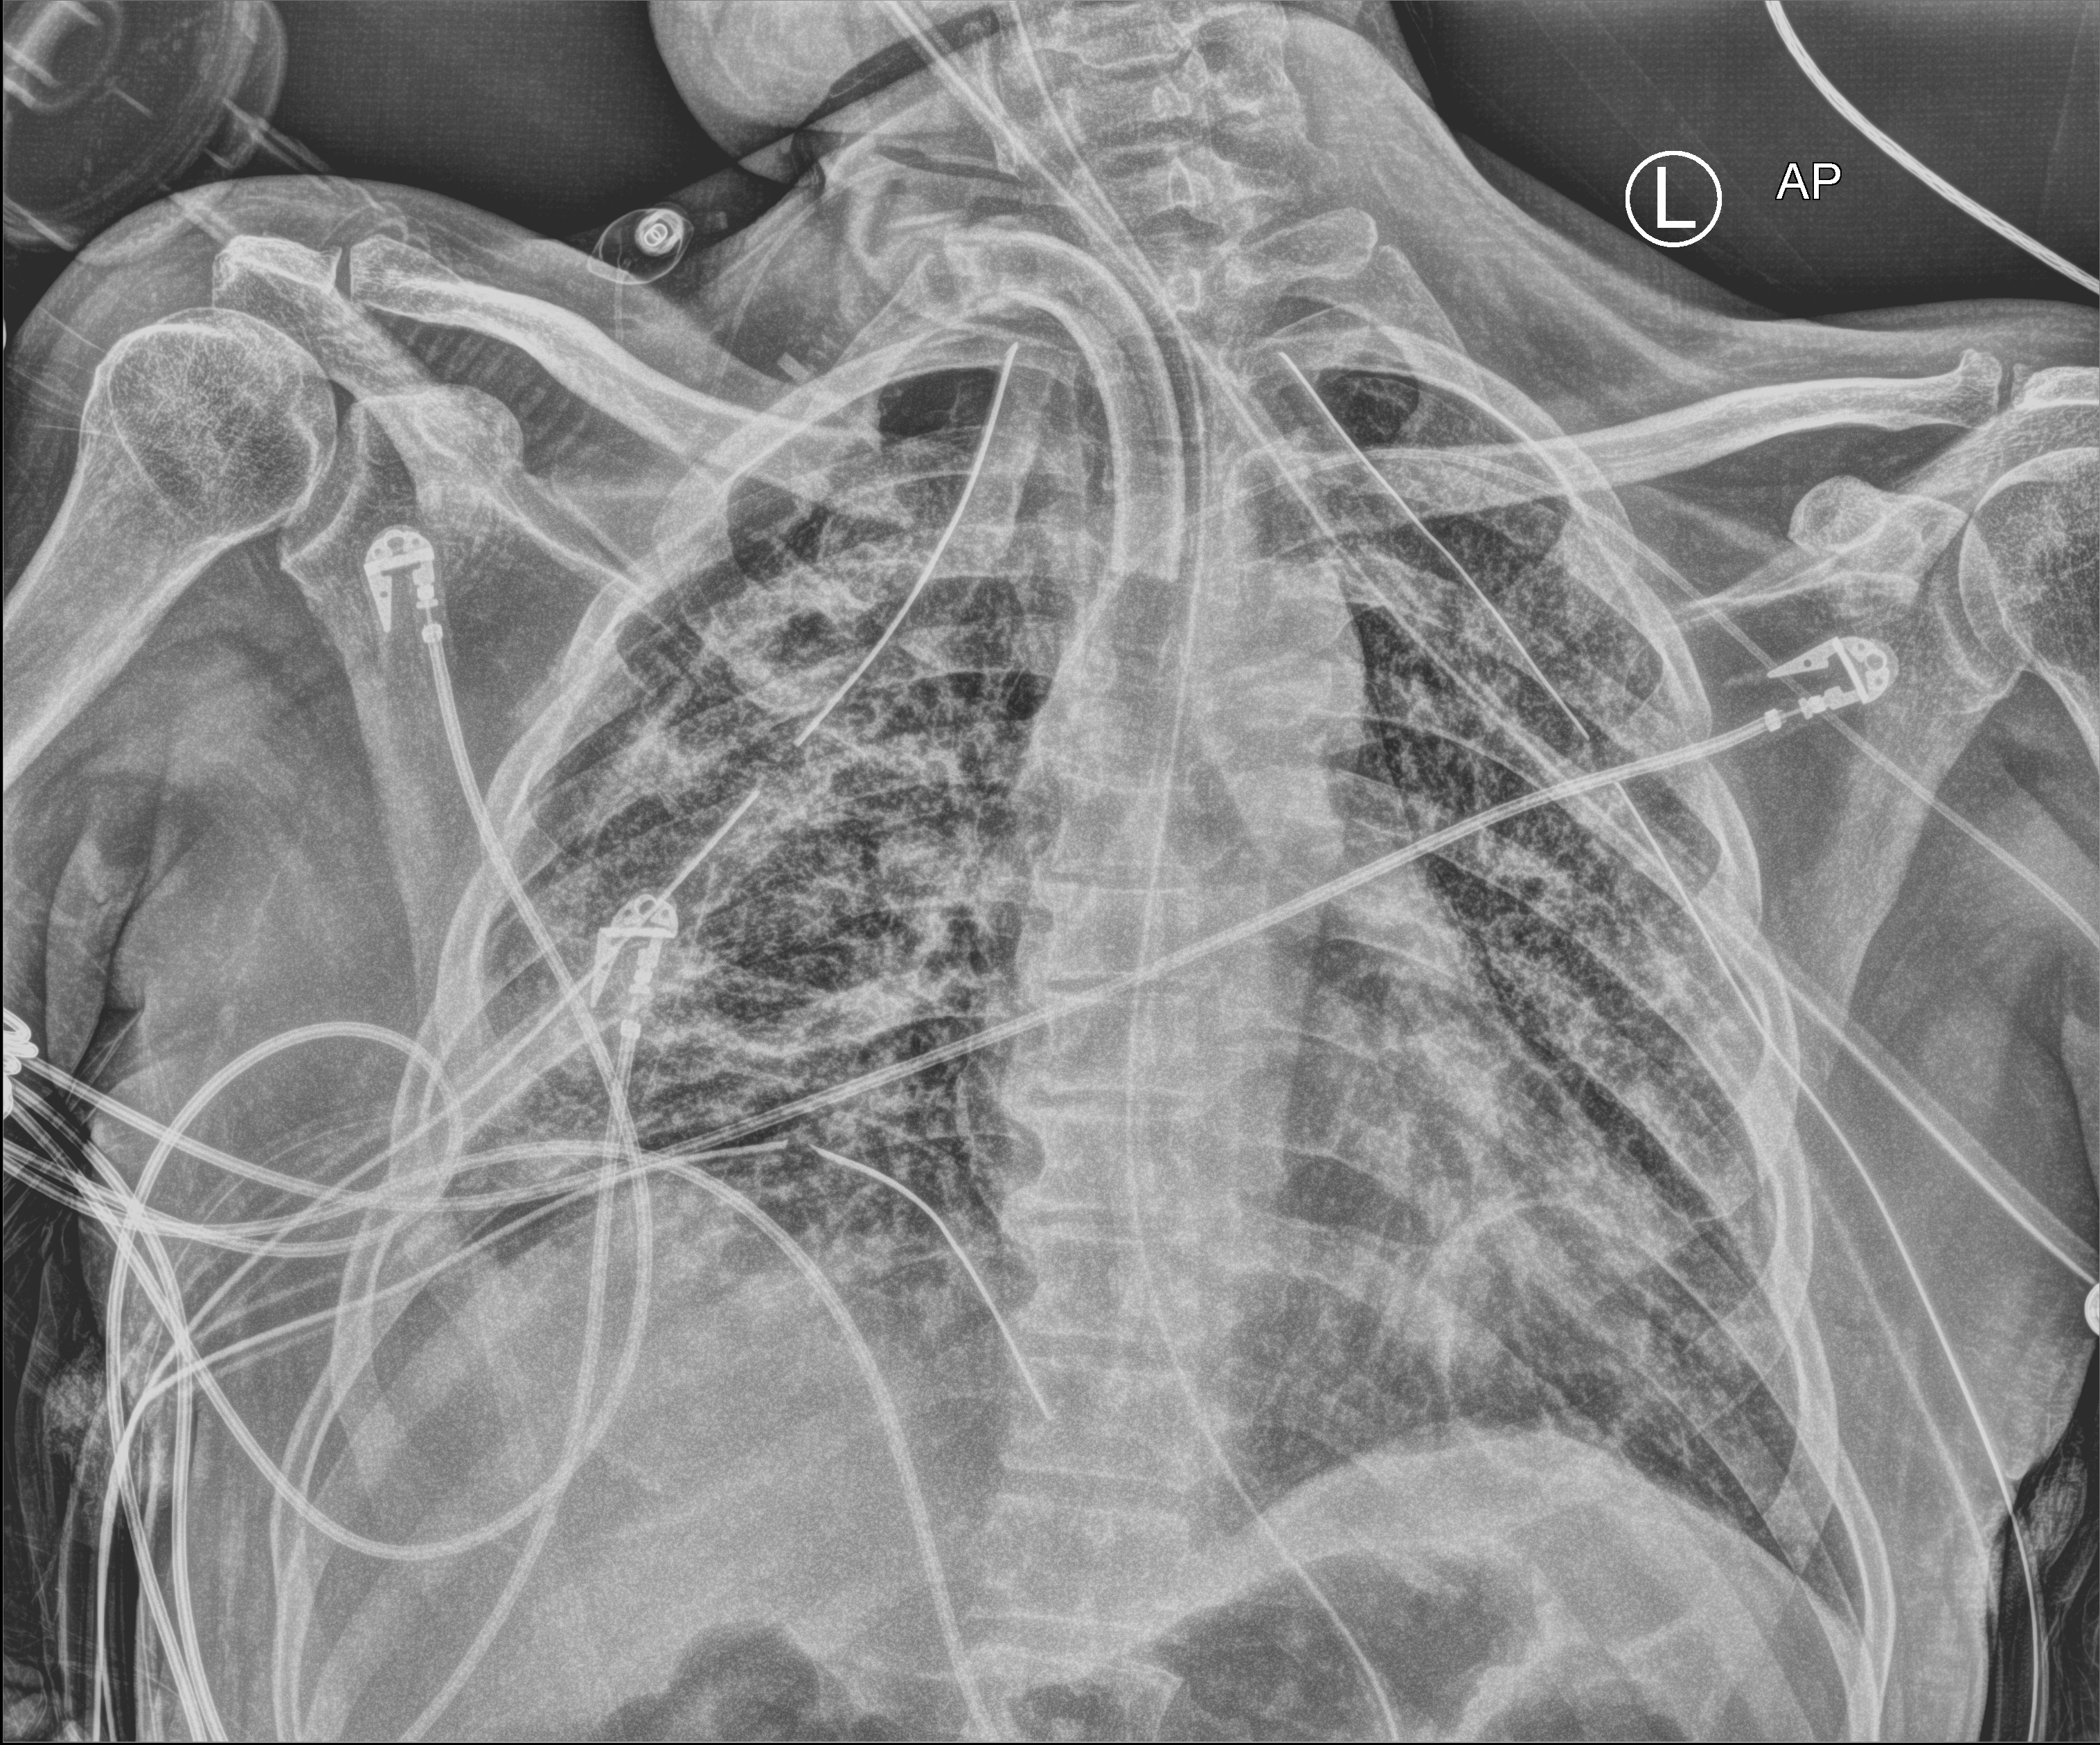
Chest X-ray (portable); anteroposterior (AP) projection. Patient hospitalised with COVID-19; male, aged 18–59 years.
Hospital-stay facts (about this admission, not read from this image; timing relative to this image not recorded): admitted to intensive care during this hospital stay: yes.